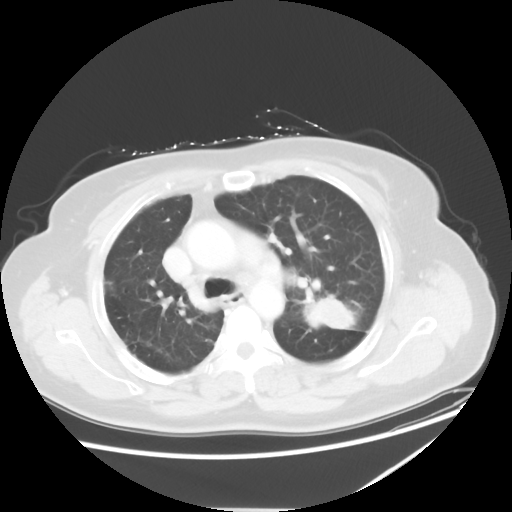
Chest CT, one axial slice. Slice 37 of 54 in the series (ordered by position). Reconstruction kernel STANDARD. 120 kVp. Lung window (W 1500 / L -600 HU). 5 mm slice thickness. 512 × 512 image matrix, field of view 384 × 384 mm. Patient: female, 61 years. From the clinical record (not read from this slice): clinical TNM (as recorded): T1c N3 M1.
Annotated regions visible in this slice (rectangle marked by the reading radiologist):
- lung tumour (recorded histology: adenocarcinoma): bounding box [x1, y1, x2, y2] px = [303, 293, 360, 335]